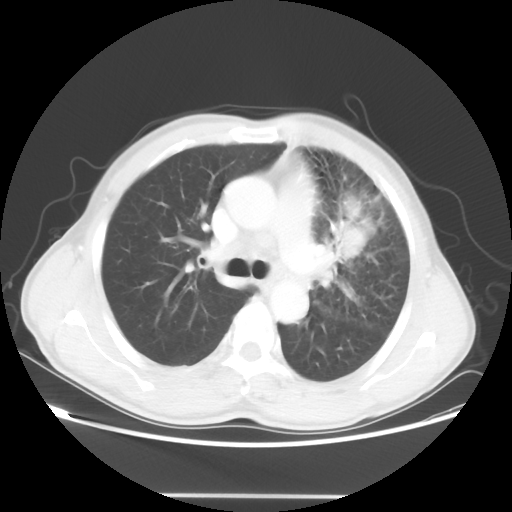
Chest CT, one axial slice. Slice 34 of 55 in the series (ordered by position). 100 kVp. Lung window (W 1500 / L -600 HU). 512 × 512 image matrix. Male patient, age 60 years. From the clinical record (not read from this slice): clinical TNM (as recorded): T3 N3 M0.
Outlined on this slice (rectangle marked by the reading radiologist):
- lung tumour (recorded histology: adenocarcinoma): bounding box (x1, y1, x2, y2) in pixels: (331, 215, 368, 268)